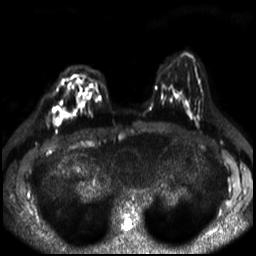
Breast MRI, one axial slice. Slice 14 of 30 in the series (ordered by position). Diffusion-weighted series; image 2 of 4 stored at this slice position (different b-values; order by instance number). 3 T. 4 mm slice thickness. 256 × 256 image matrix, field of view 320 × 320 mm. Female patient.
Outlined on this slice (manually delineated by an expert):
- tumour on diffusion-weighted imaging: bounding box (x1, y1, x2, y2) in pixels: (56, 111, 65, 121)